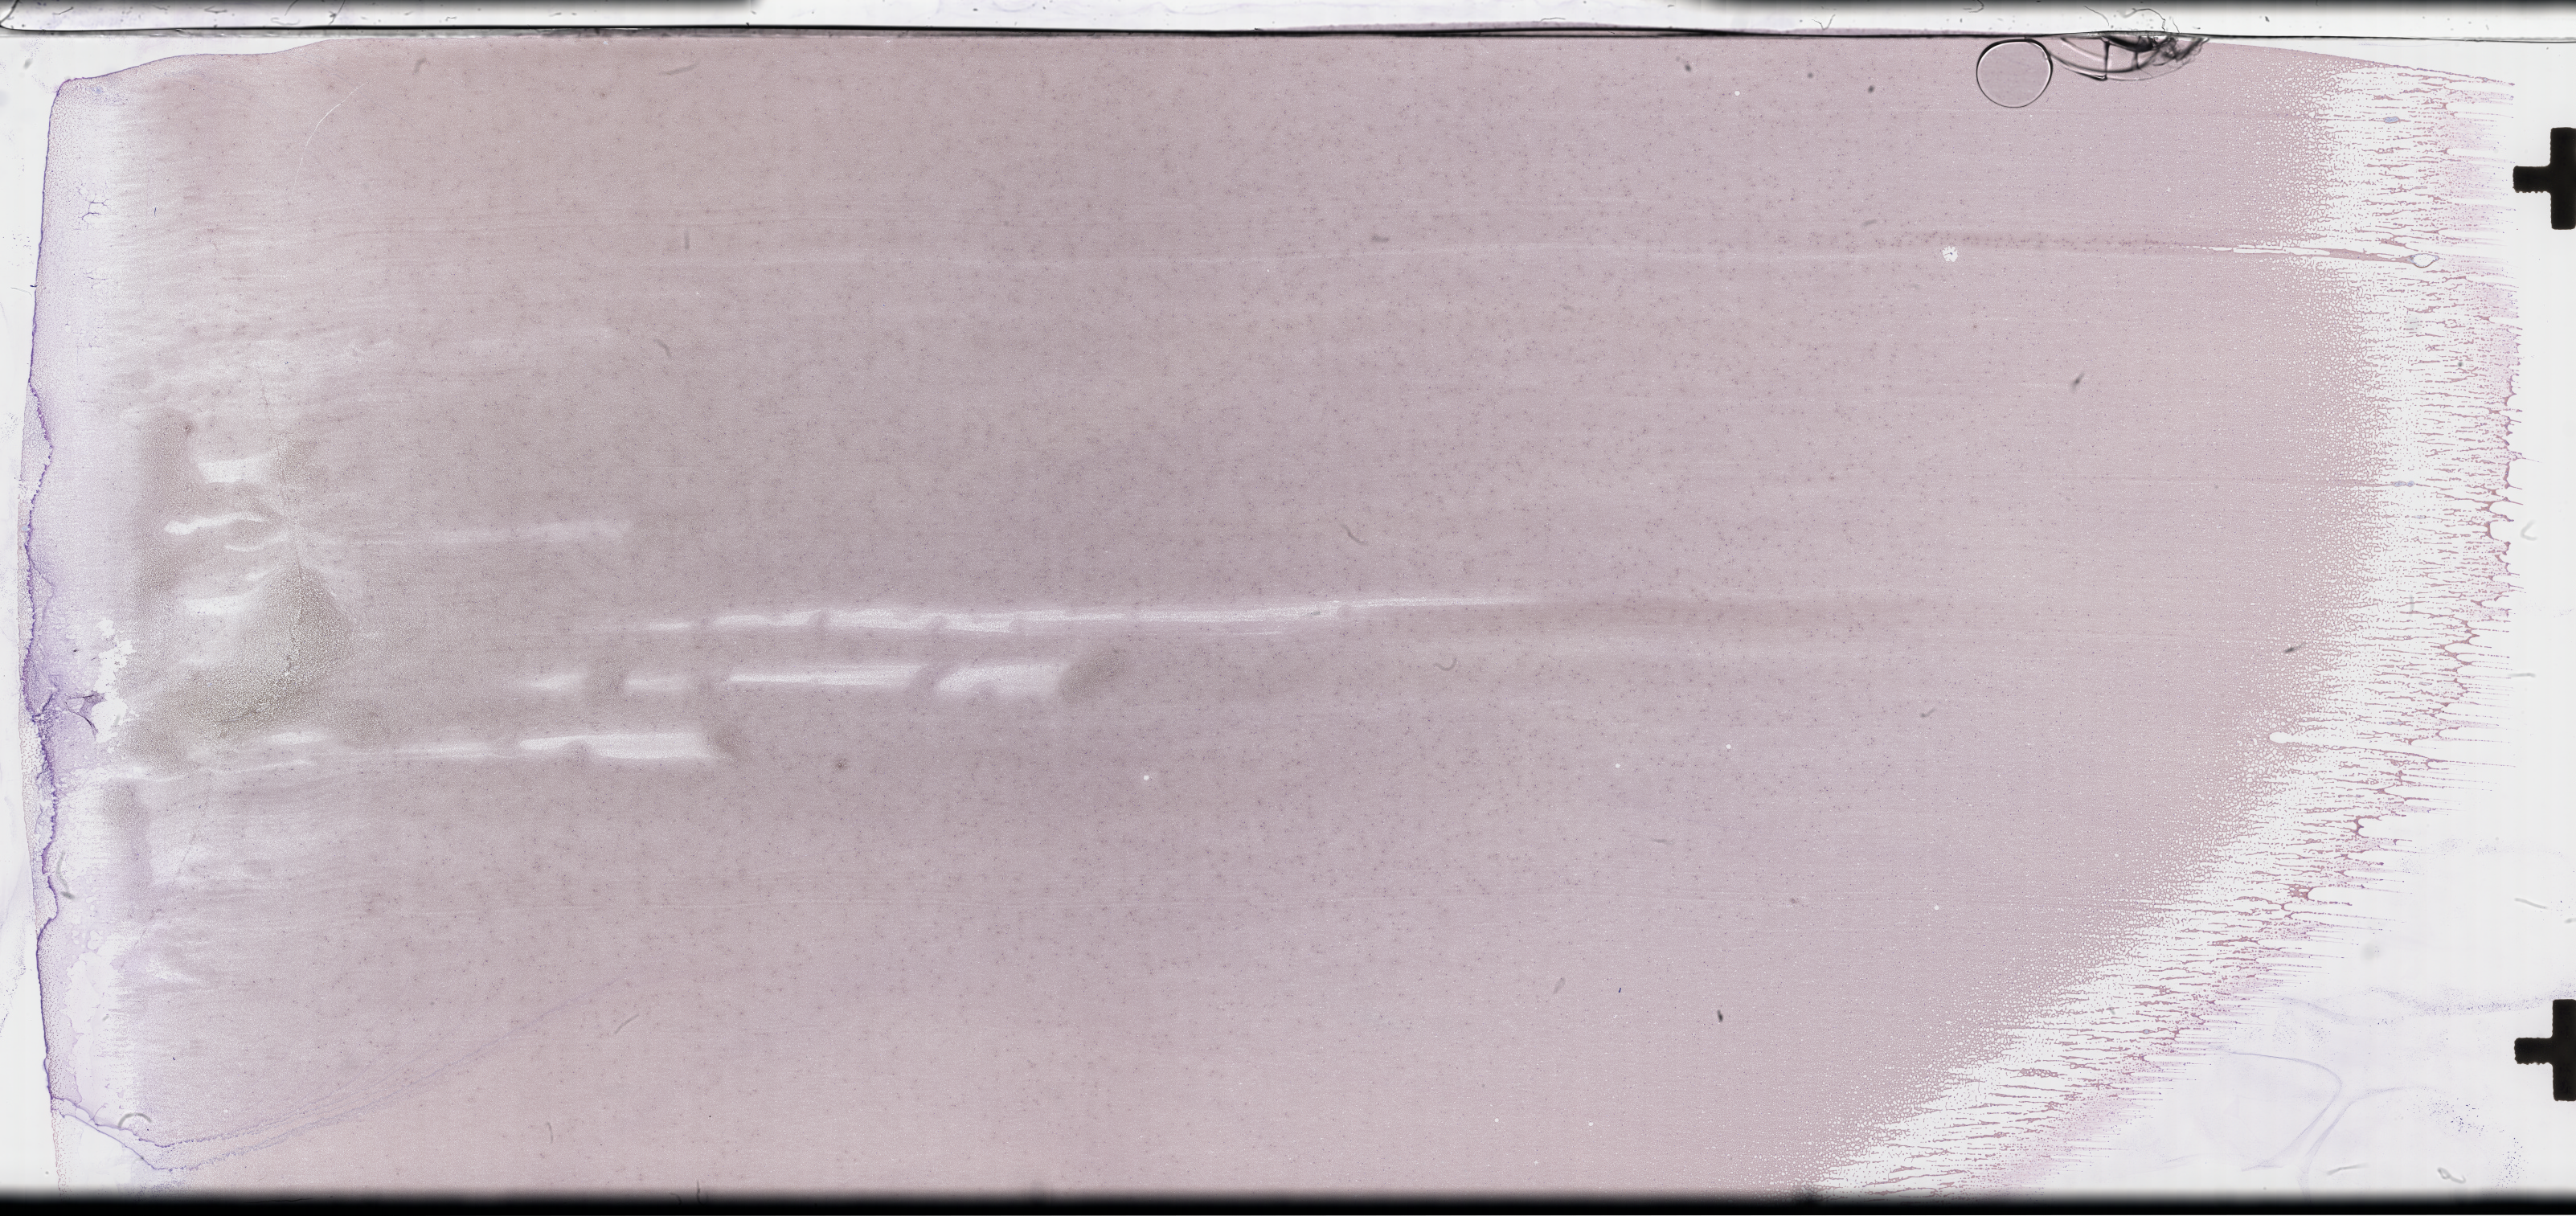
Wright-Giemsa-stained whole blood smear, whole-slide image — a low-resolution overview of the entire scanned area, about 51.8 x 24.4 mm. Patient sex: male.
From a patient with: Acute Myeloid Leukemia Not Otherwise Specified.